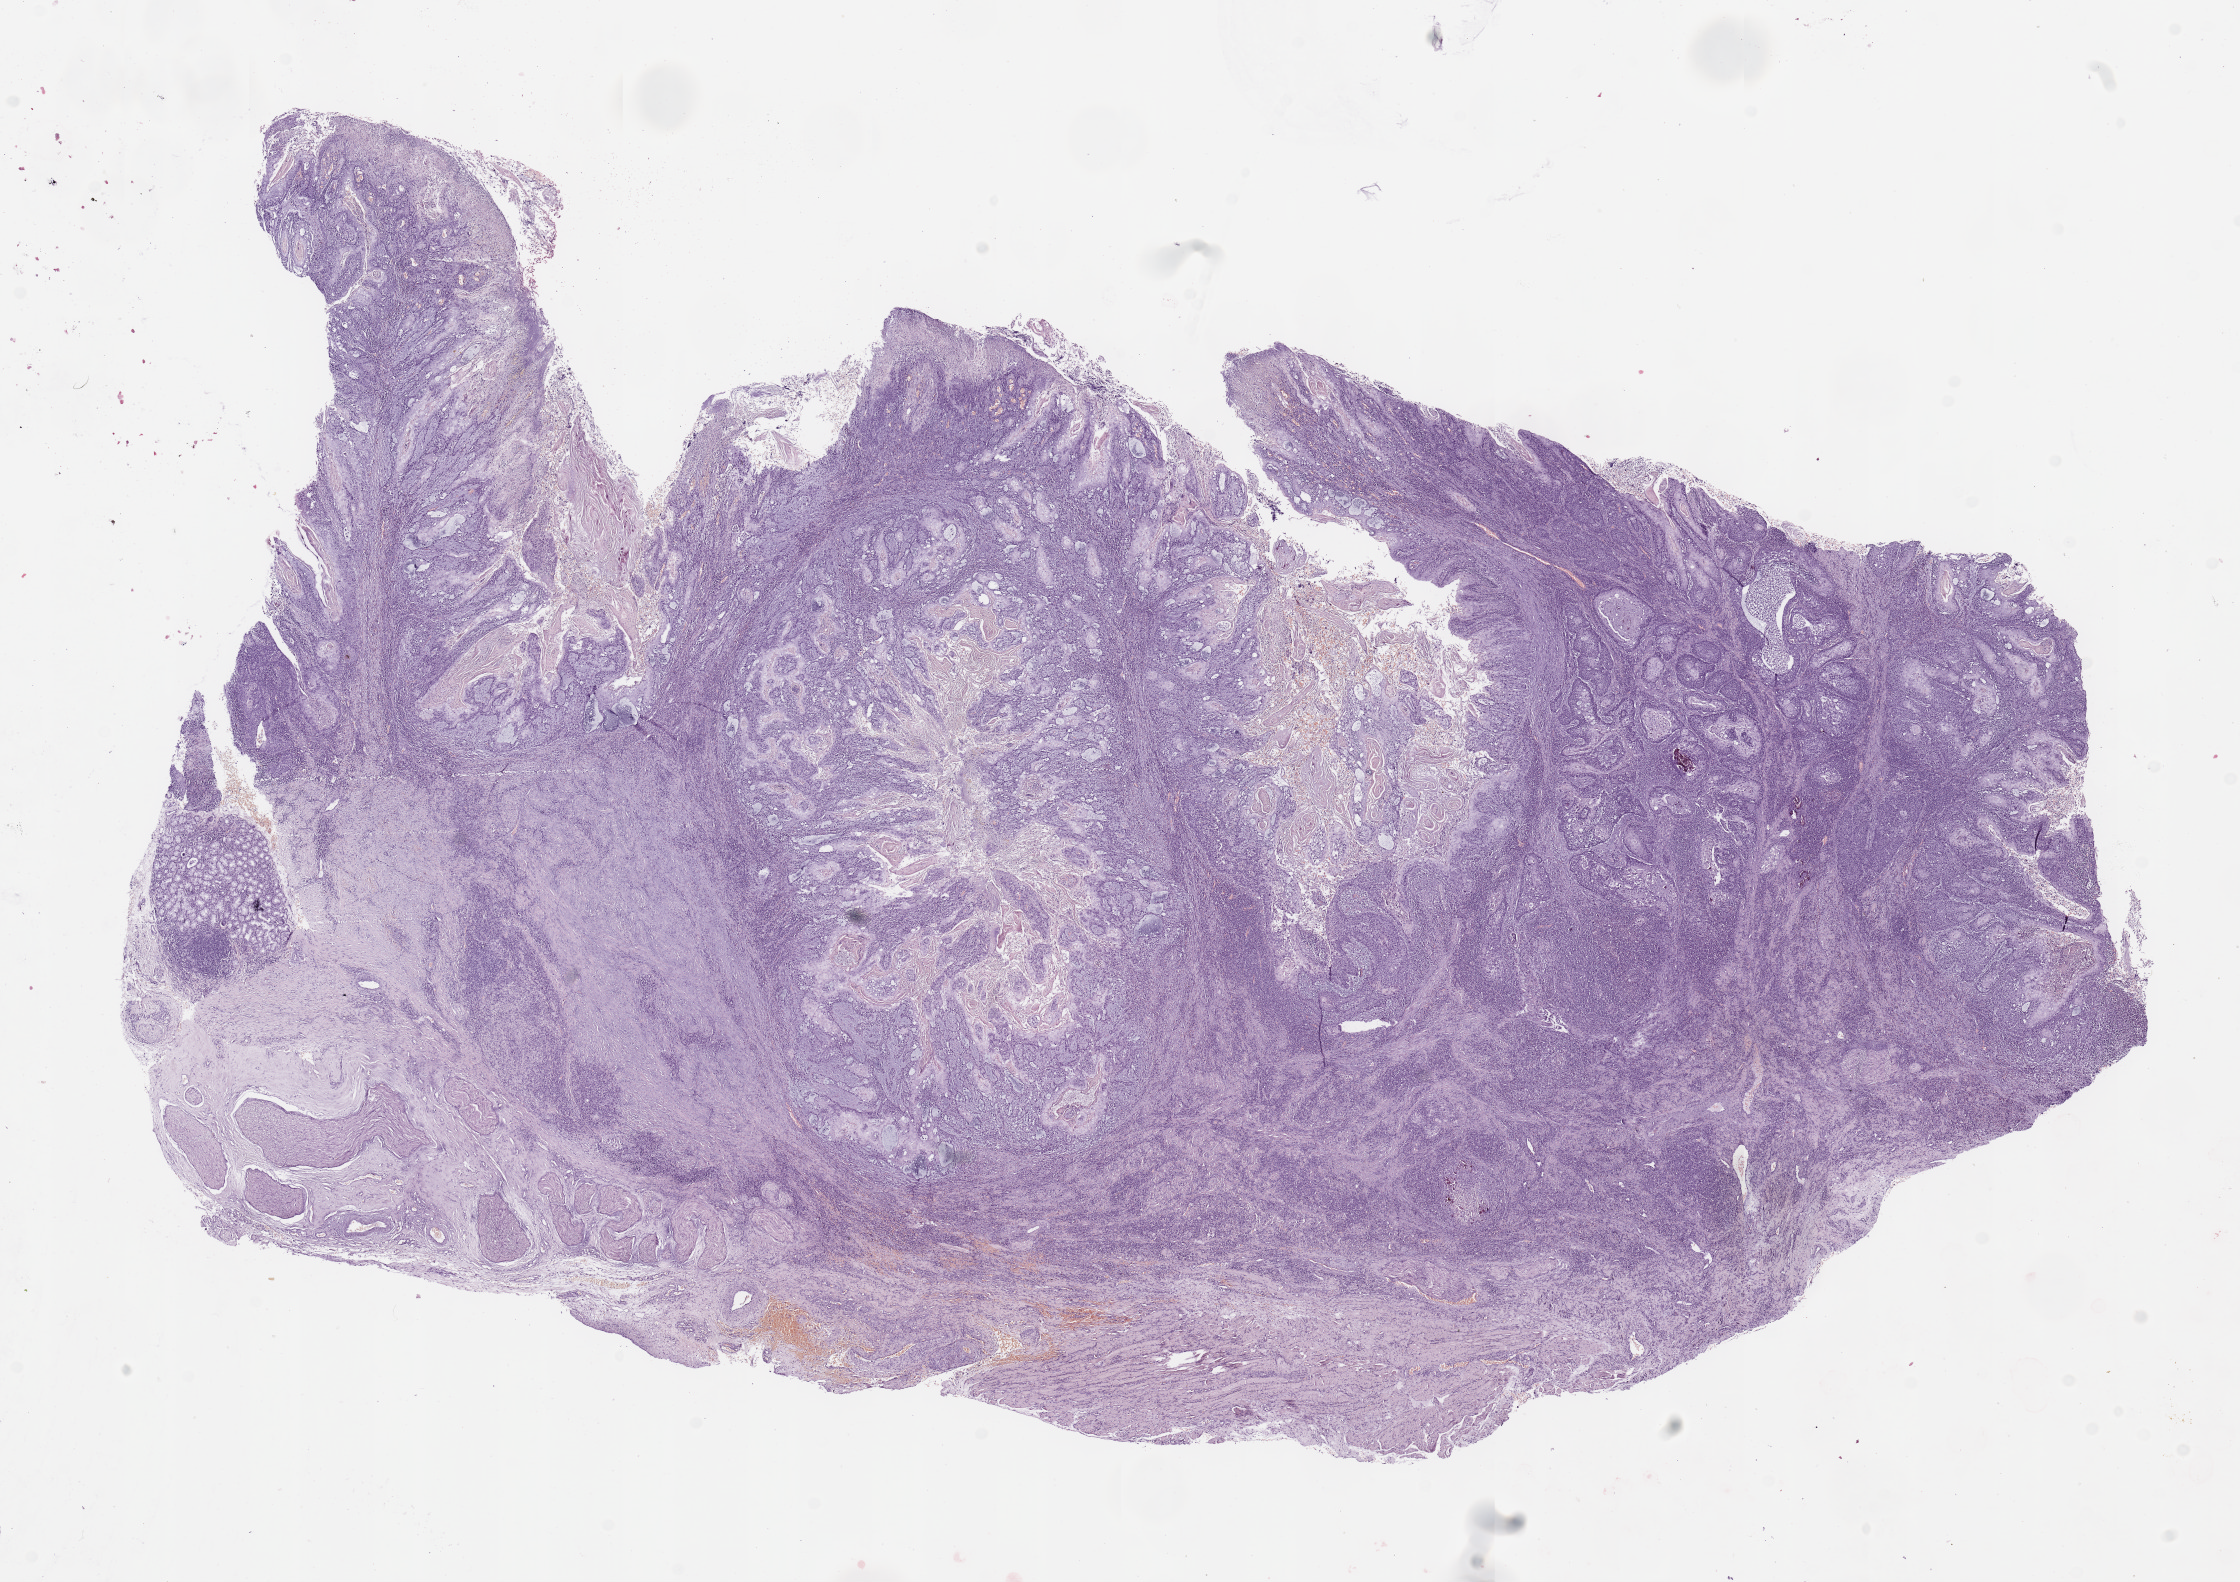
Digitized H&E tissue section (whole slide), low-resolution overview of the scanned area, about 17.7 x 12.5 mm (acquisition: 20x scan); tumour tissue sample, sampled site: tongue. 59-year-old male patient. Histologic grade: G2 (moderately differentiated). Composition of this section per pathologist review: tumour nuclei 85%, necrosis 5%.
Primary tumour site (as recorded): oral cavity. AJCC pathologic stage: II. Histologic diagnosis: Squamous cell carcinoma, NOS (tongue, NOS).